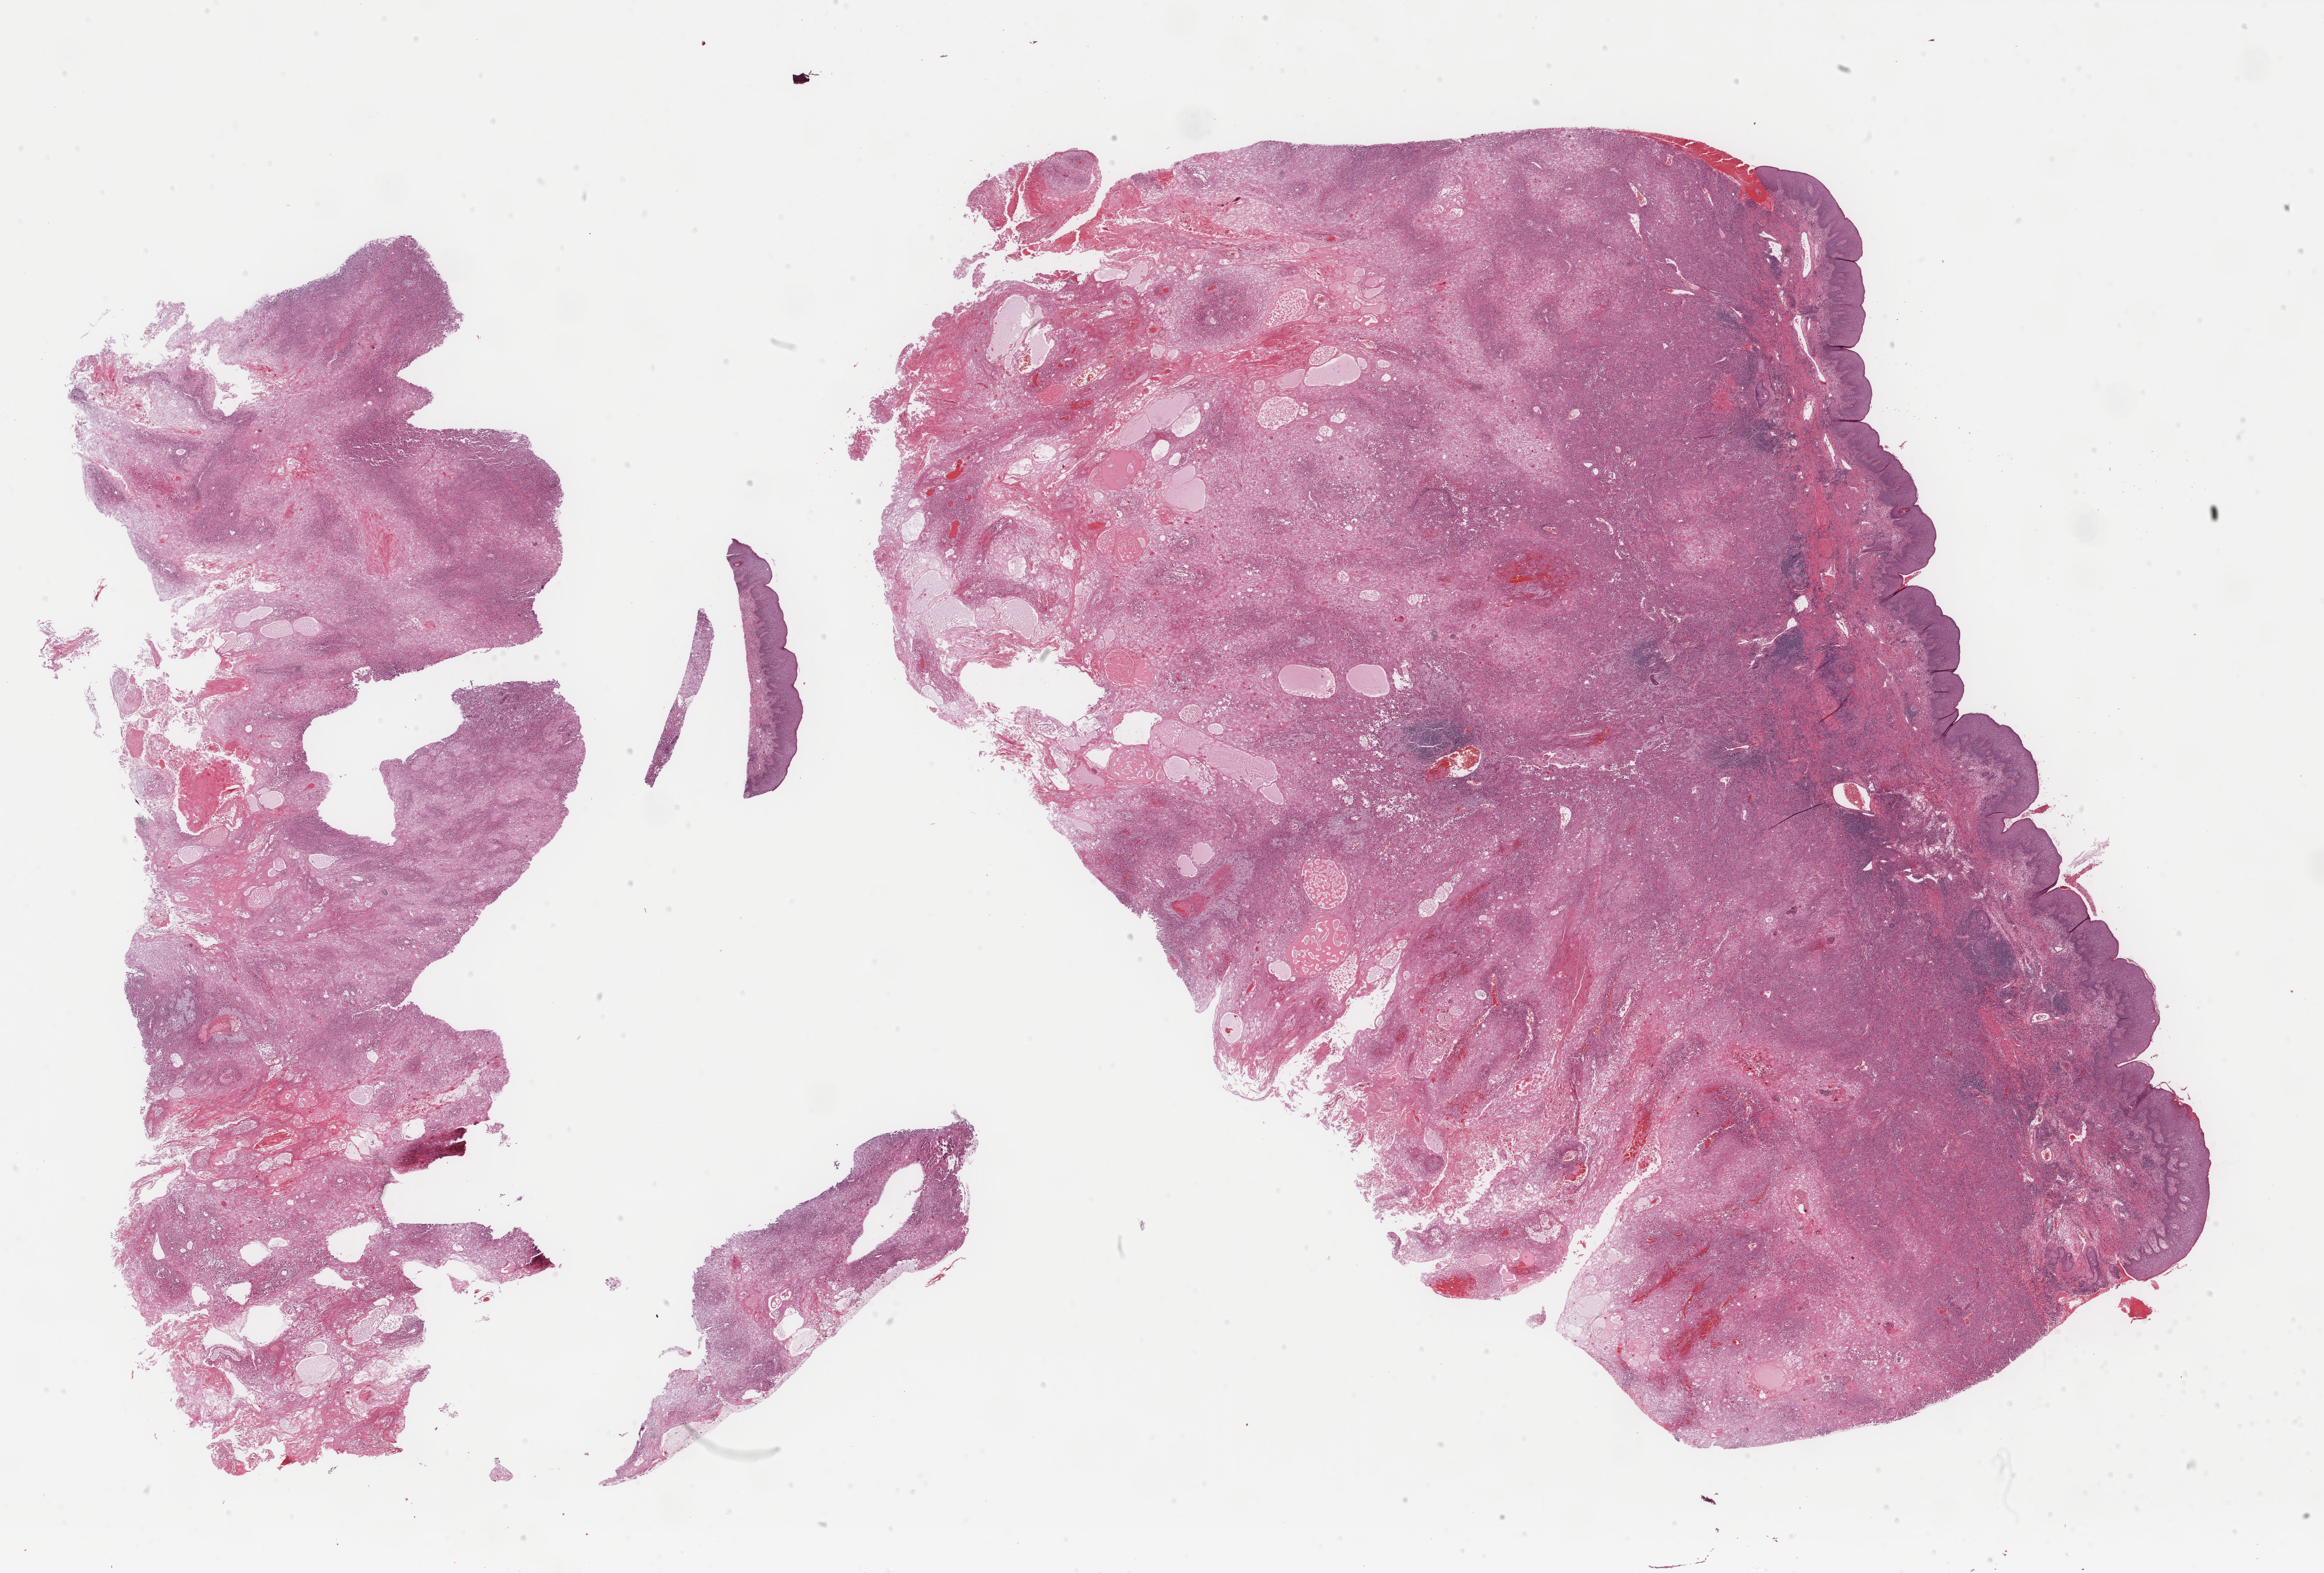
Whole-slide histology image, H&E-stained — low-resolution overview of the scanned area, about 31.9 x 21.6 mm. FFPE section. Sample: primary tumour, breast. Female patient; age at initial diagnosis 68 years.
Diagnosis: Metaplastic carcinoma, NOS. Lymph nodes positive (case pathology): 1 of 24 examined. TNM: T3 N1 M0. AJCC pathologic stage: IIIA (7th edition). Laterality: right.